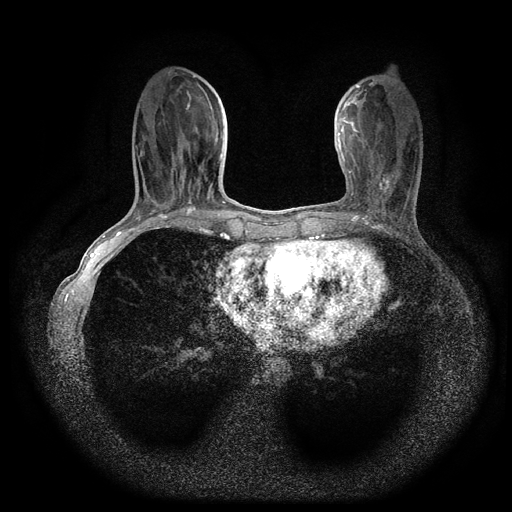
Breast MRI (dynamic contrast-enhanced, multi-phase), one axial slice; slice 35 of 116 in the series (ordered by position); dynamic contrast-enhanced series, time point 2 of 5 at this slice position (early post-contrast); 1.5 T; TE 2.7 ms, TR 5.4 ms; 2 mm slice thickness; 512 × 512 image matrix, field of view 330 × 330 mm. Patient: female, 49 years.
Outlined on this slice (semi-automatically segmented with operator editing):
- breast lesion (labelled 'tumour' in the annotation; benign lesions carry a separate 'benign' label): box from (x=375, y=173) to (x=392, y=195) px